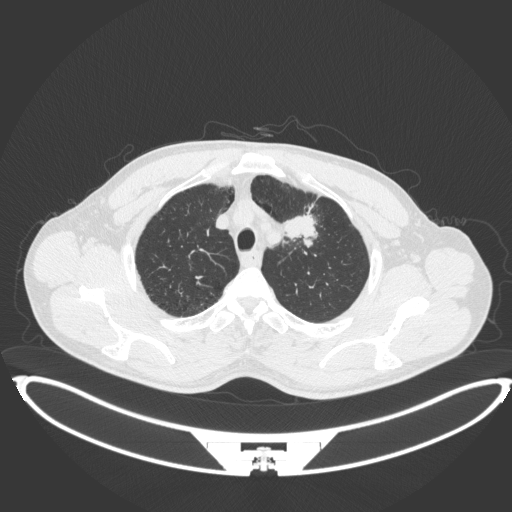
Chest CT, one axial slice; position 364 of 407 along the scan axis; 120 kVp; lung window (W 1500 / L -600 HU); 1 mm slice thickness; 512 × 512 image matrix. Patient: male, 60 years. From the clinical record (not read from this slice): clinical TNM (as recorded): T2a N0 M0; histopathological grade: G1-G2.
Structures marked on this image (bounding box drawn by a radiologist):
- lung tumour (recorded histology: squamous cell carcinoma): box from (x=280, y=211) to (x=319, y=249) px